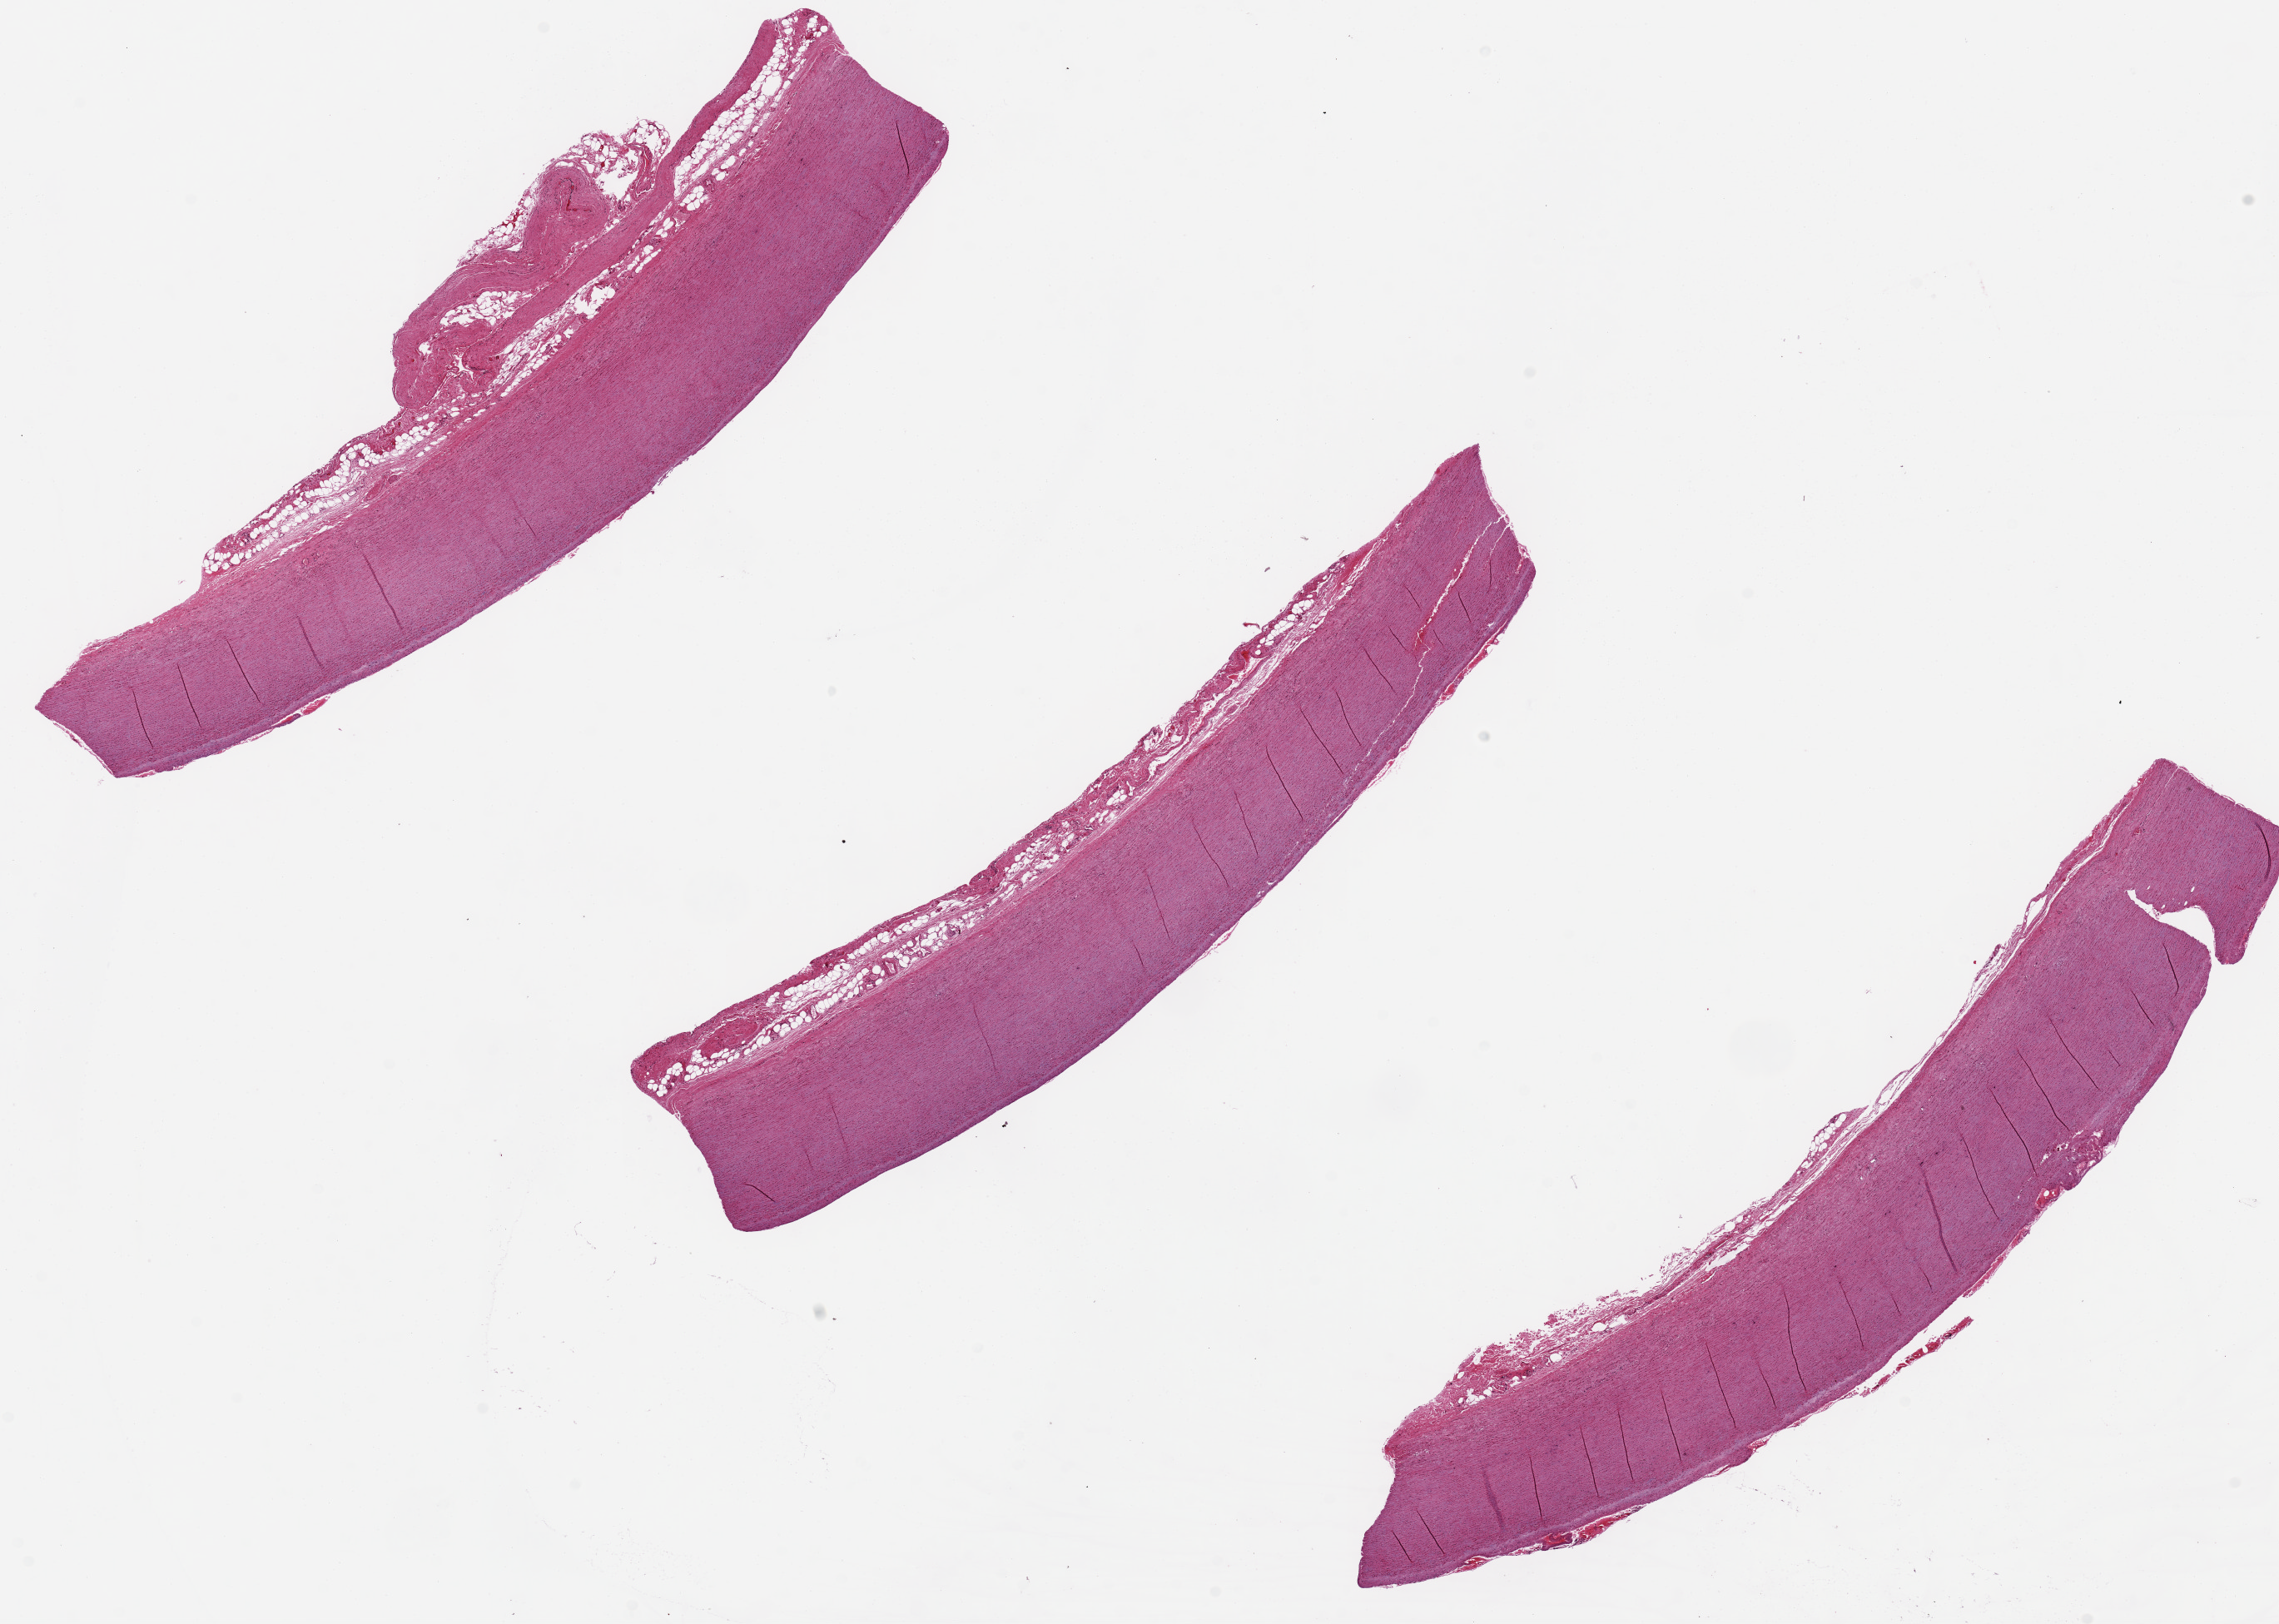
Whole-slide image, hematoxylin and eosin (H&E) stain, brightfield, a low-resolution overview of the entire scanned area, about 21.7 x 15.4 mm, PAXgene-fixed paraffin-embedded (PFPE) section, section of aorta (target tissue), tissue donor sample. Donor sex: female.
Reviewer comment on this tissue sample: 3 pieces,11x2mm.